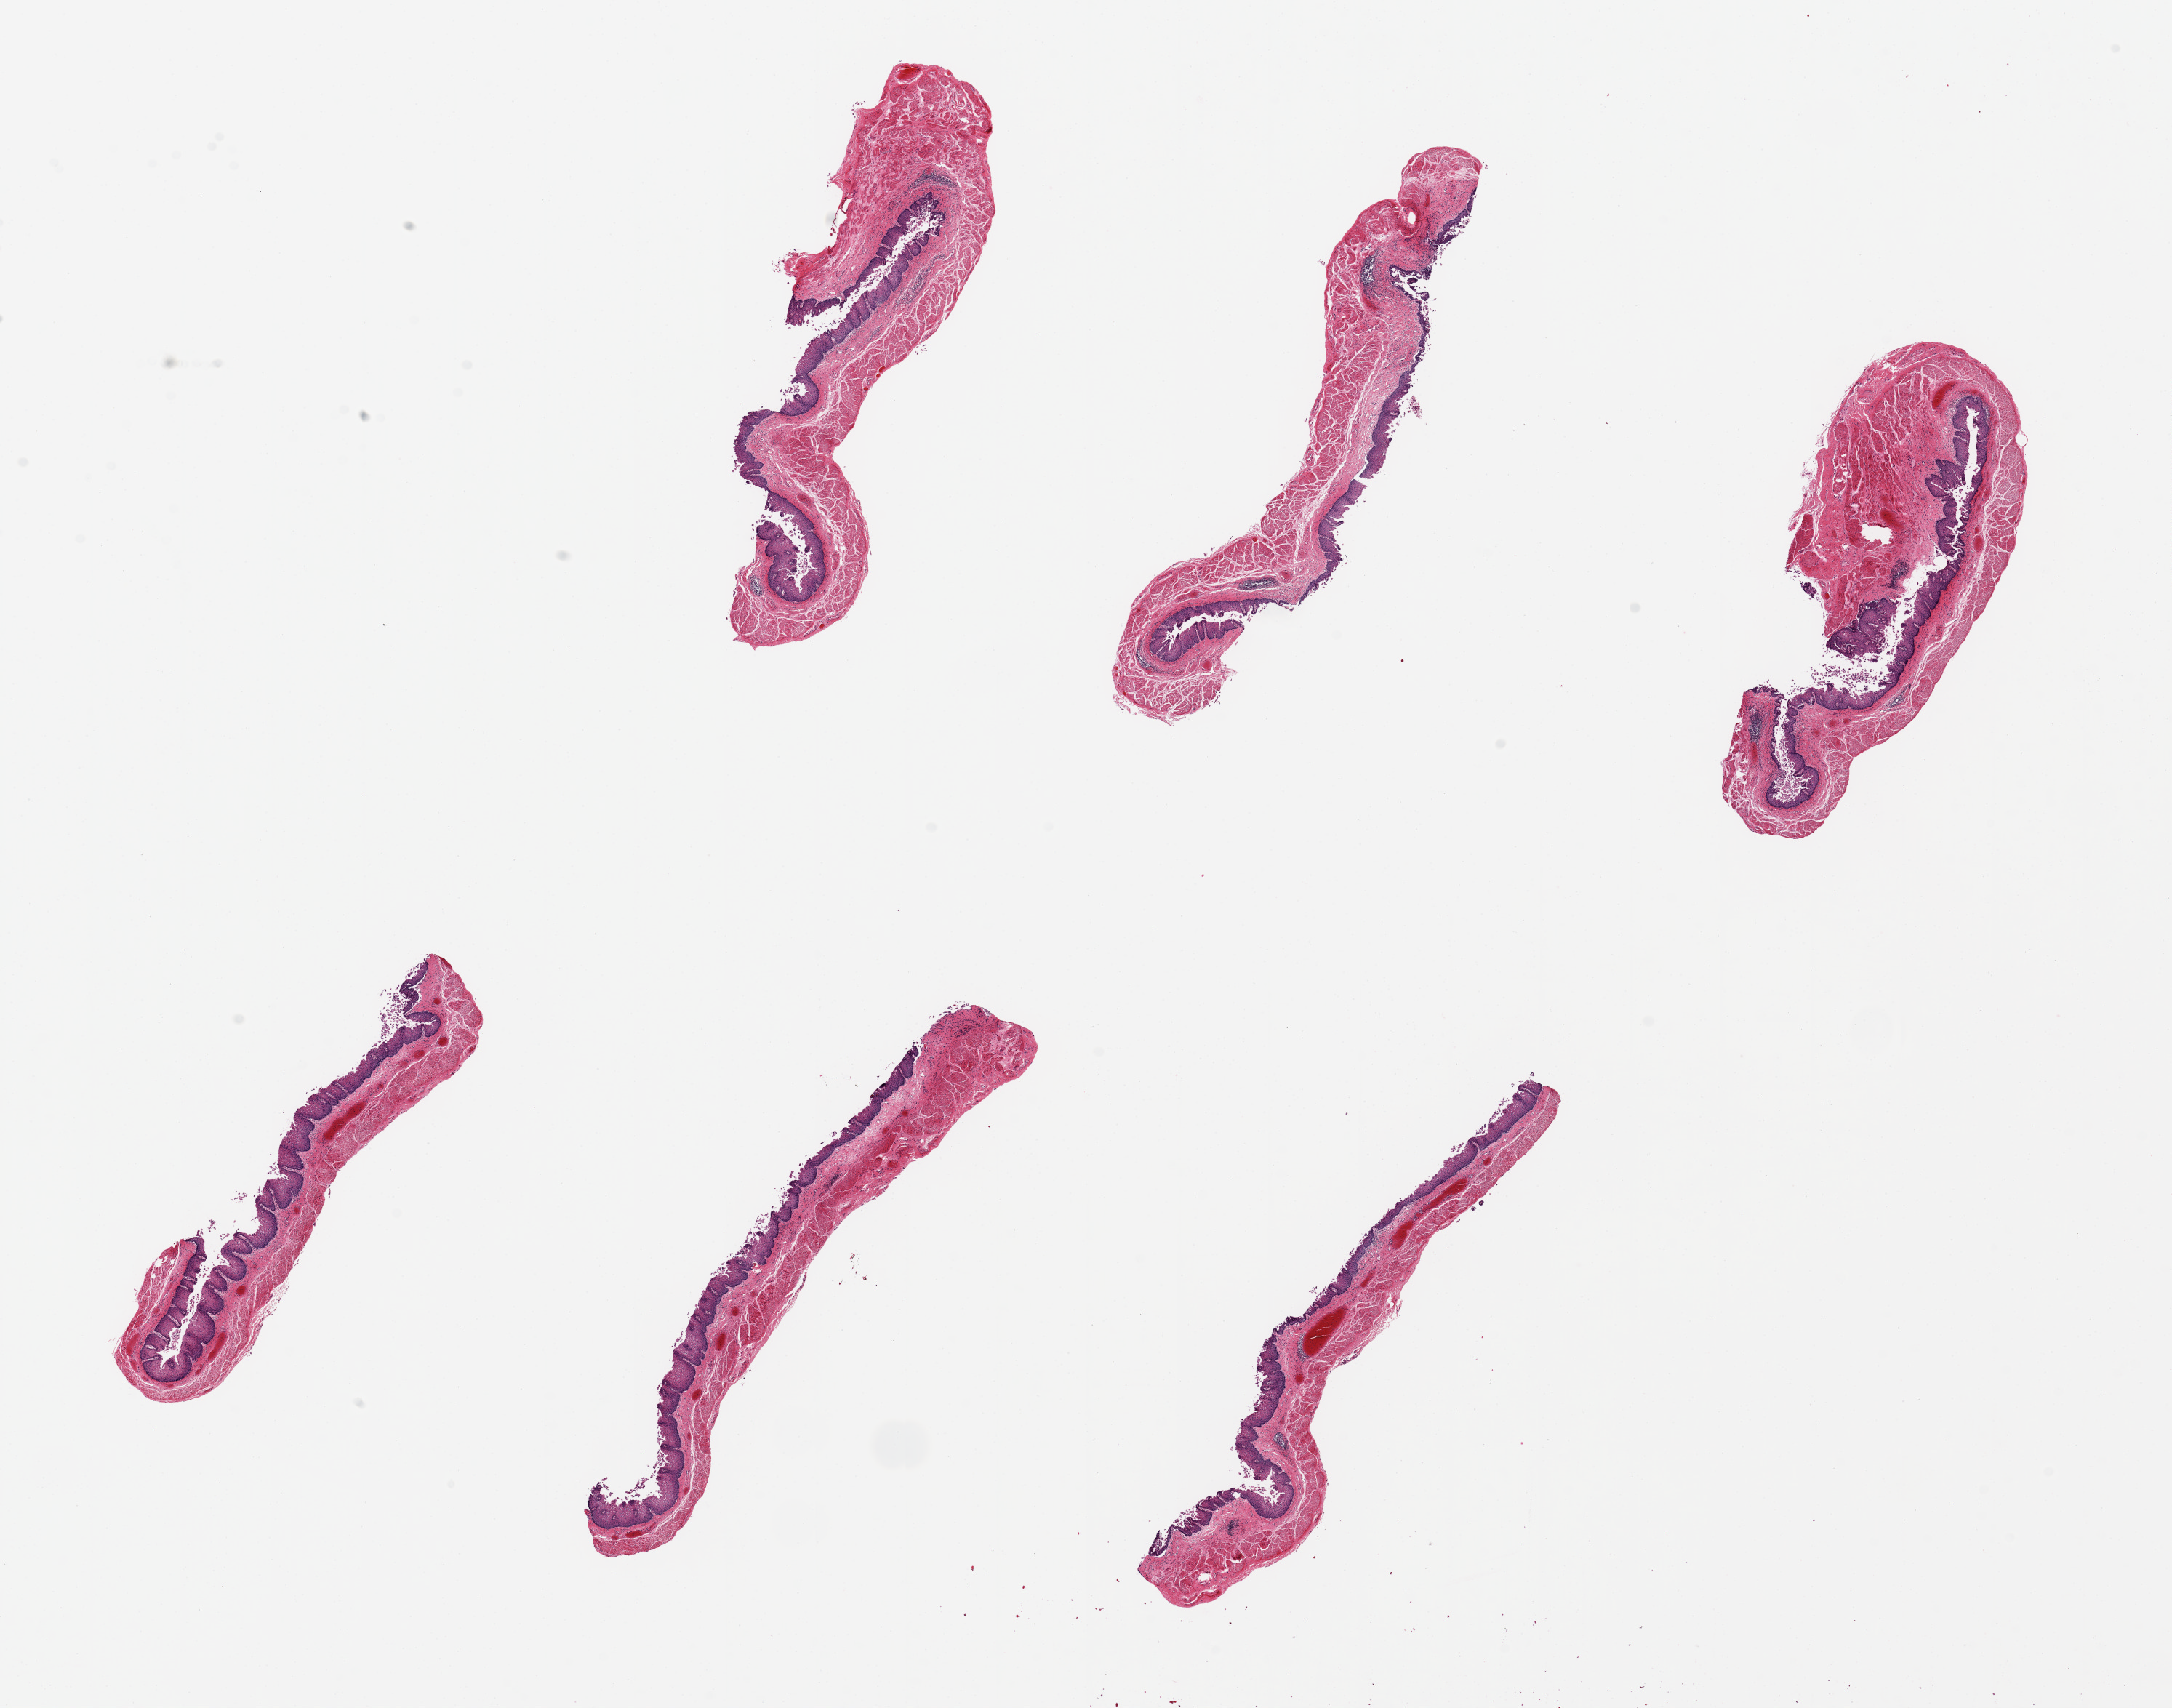
H&E whole-slide image — whole scanned area (about 23.6 x 18.6 mm) shown as a low-resolution overview; PAXgene-fixed, paraffin-embedded tissue; target tissue: esophageal mucous membrane; donor tissue sample. Donor: female.
- pathologist's review note for this sample: 6 pieces ~7x1mm, Squamous mucosa sloughing, ~10% thickness, unusually poorly preserved